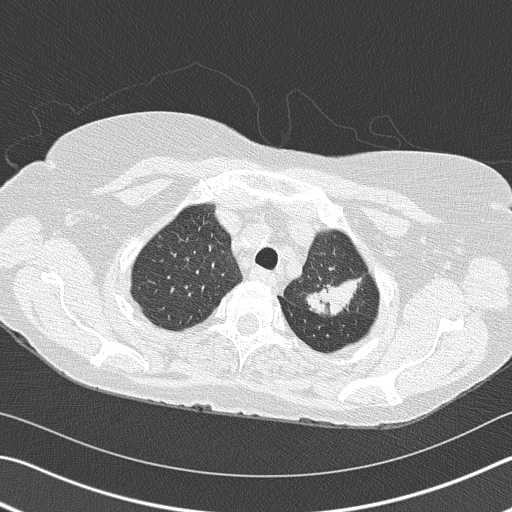
Low-dose screening chest CT, axial slice. Second annual screen. Lung window (W 1500 / L -600 HU). 512 × 512 image matrix, field of view 342 × 342 mm. Female, age 68 years at enrolment. Former smoker at enrolment.
Expert-annotated lung lesion, box from (x=290, y=238) to (x=373, y=326) px. Screening reader's record for this exam (one nodule recorded; not confirmed to be the boxed lesion): non-calcified nodule or mass ≥4 mm, left upper lobe, 4 × 2 mm, spiculated (stellate) margins, soft tissue attenuation, pre-existing on the prior screen: yes; interval growth: yes. Participant outcome: lung cancer diagnosed 392 days after this screen (after the third annual screen) — adenocarcinoma, NOS, left upper lobe, poorly differentiated (G3), stage IB (AJCC 6th edition), 50 mm at pathology.